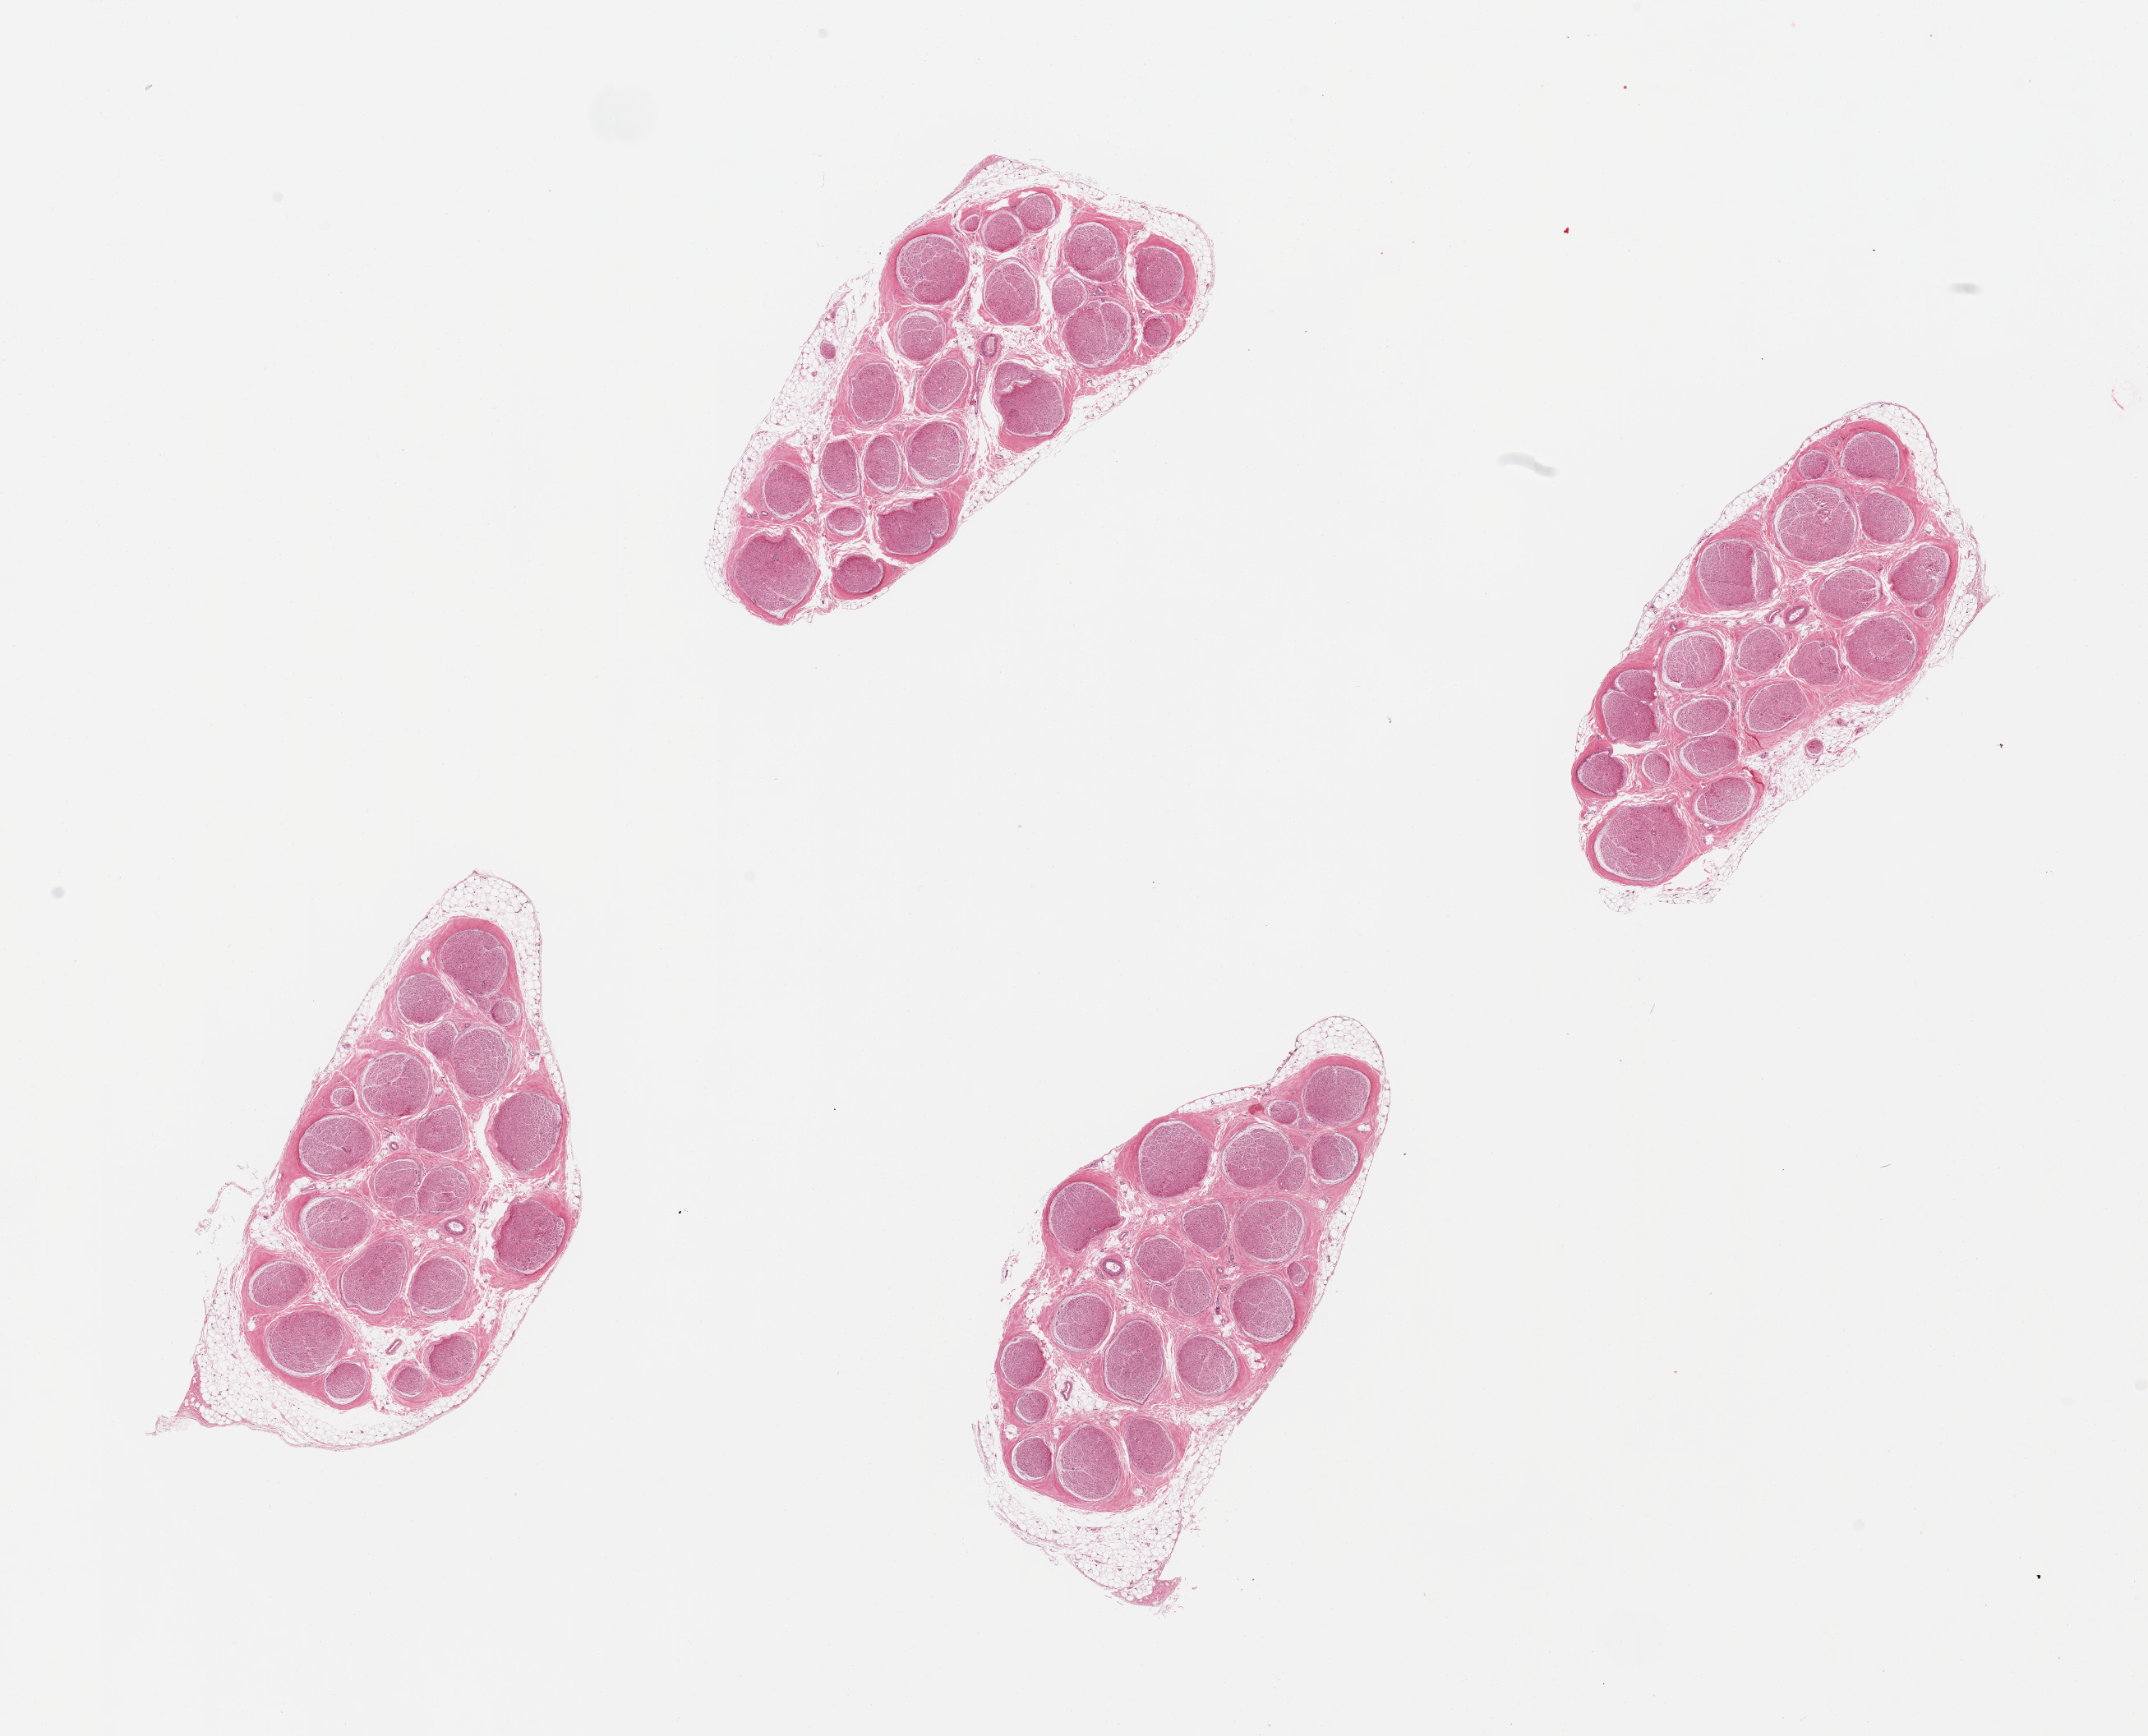
Digitized haematoxylin and eosin-stained section, a low-resolution overview of the entire scanned area, about 20.7 x 16.7 mm; PAXgene-fixed, paraffin-embedded tissue; sampled site (target tissue): tibial nerve; tissue donor sample. Donor: female.
Review note (as recorded): 4 pieces, rim of trace fat up to ~1mm.